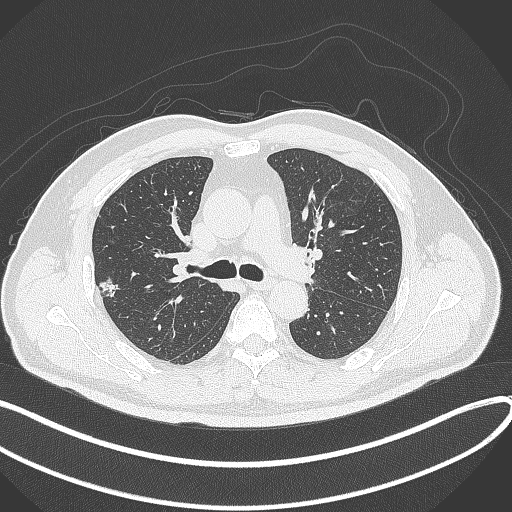
Chest CT, one axial slice; reconstruction kernel B70f; lung window (W 1500 / L -600 HU); 1 mm slice thickness; 512 × 512 image matrix, field of view 400 × 400 mm. Male patient, age 60 years. Case-level facts recorded for this patient, not image findings: clinical TNM (as recorded): T1c N0 M0.
Annotated regions visible in this slice (bounding box drawn by a radiologist):
- lung tumour (recorded histology: adenocarcinoma): bounding box <95,276,120,302> (left, top, right, bottom; pixels)